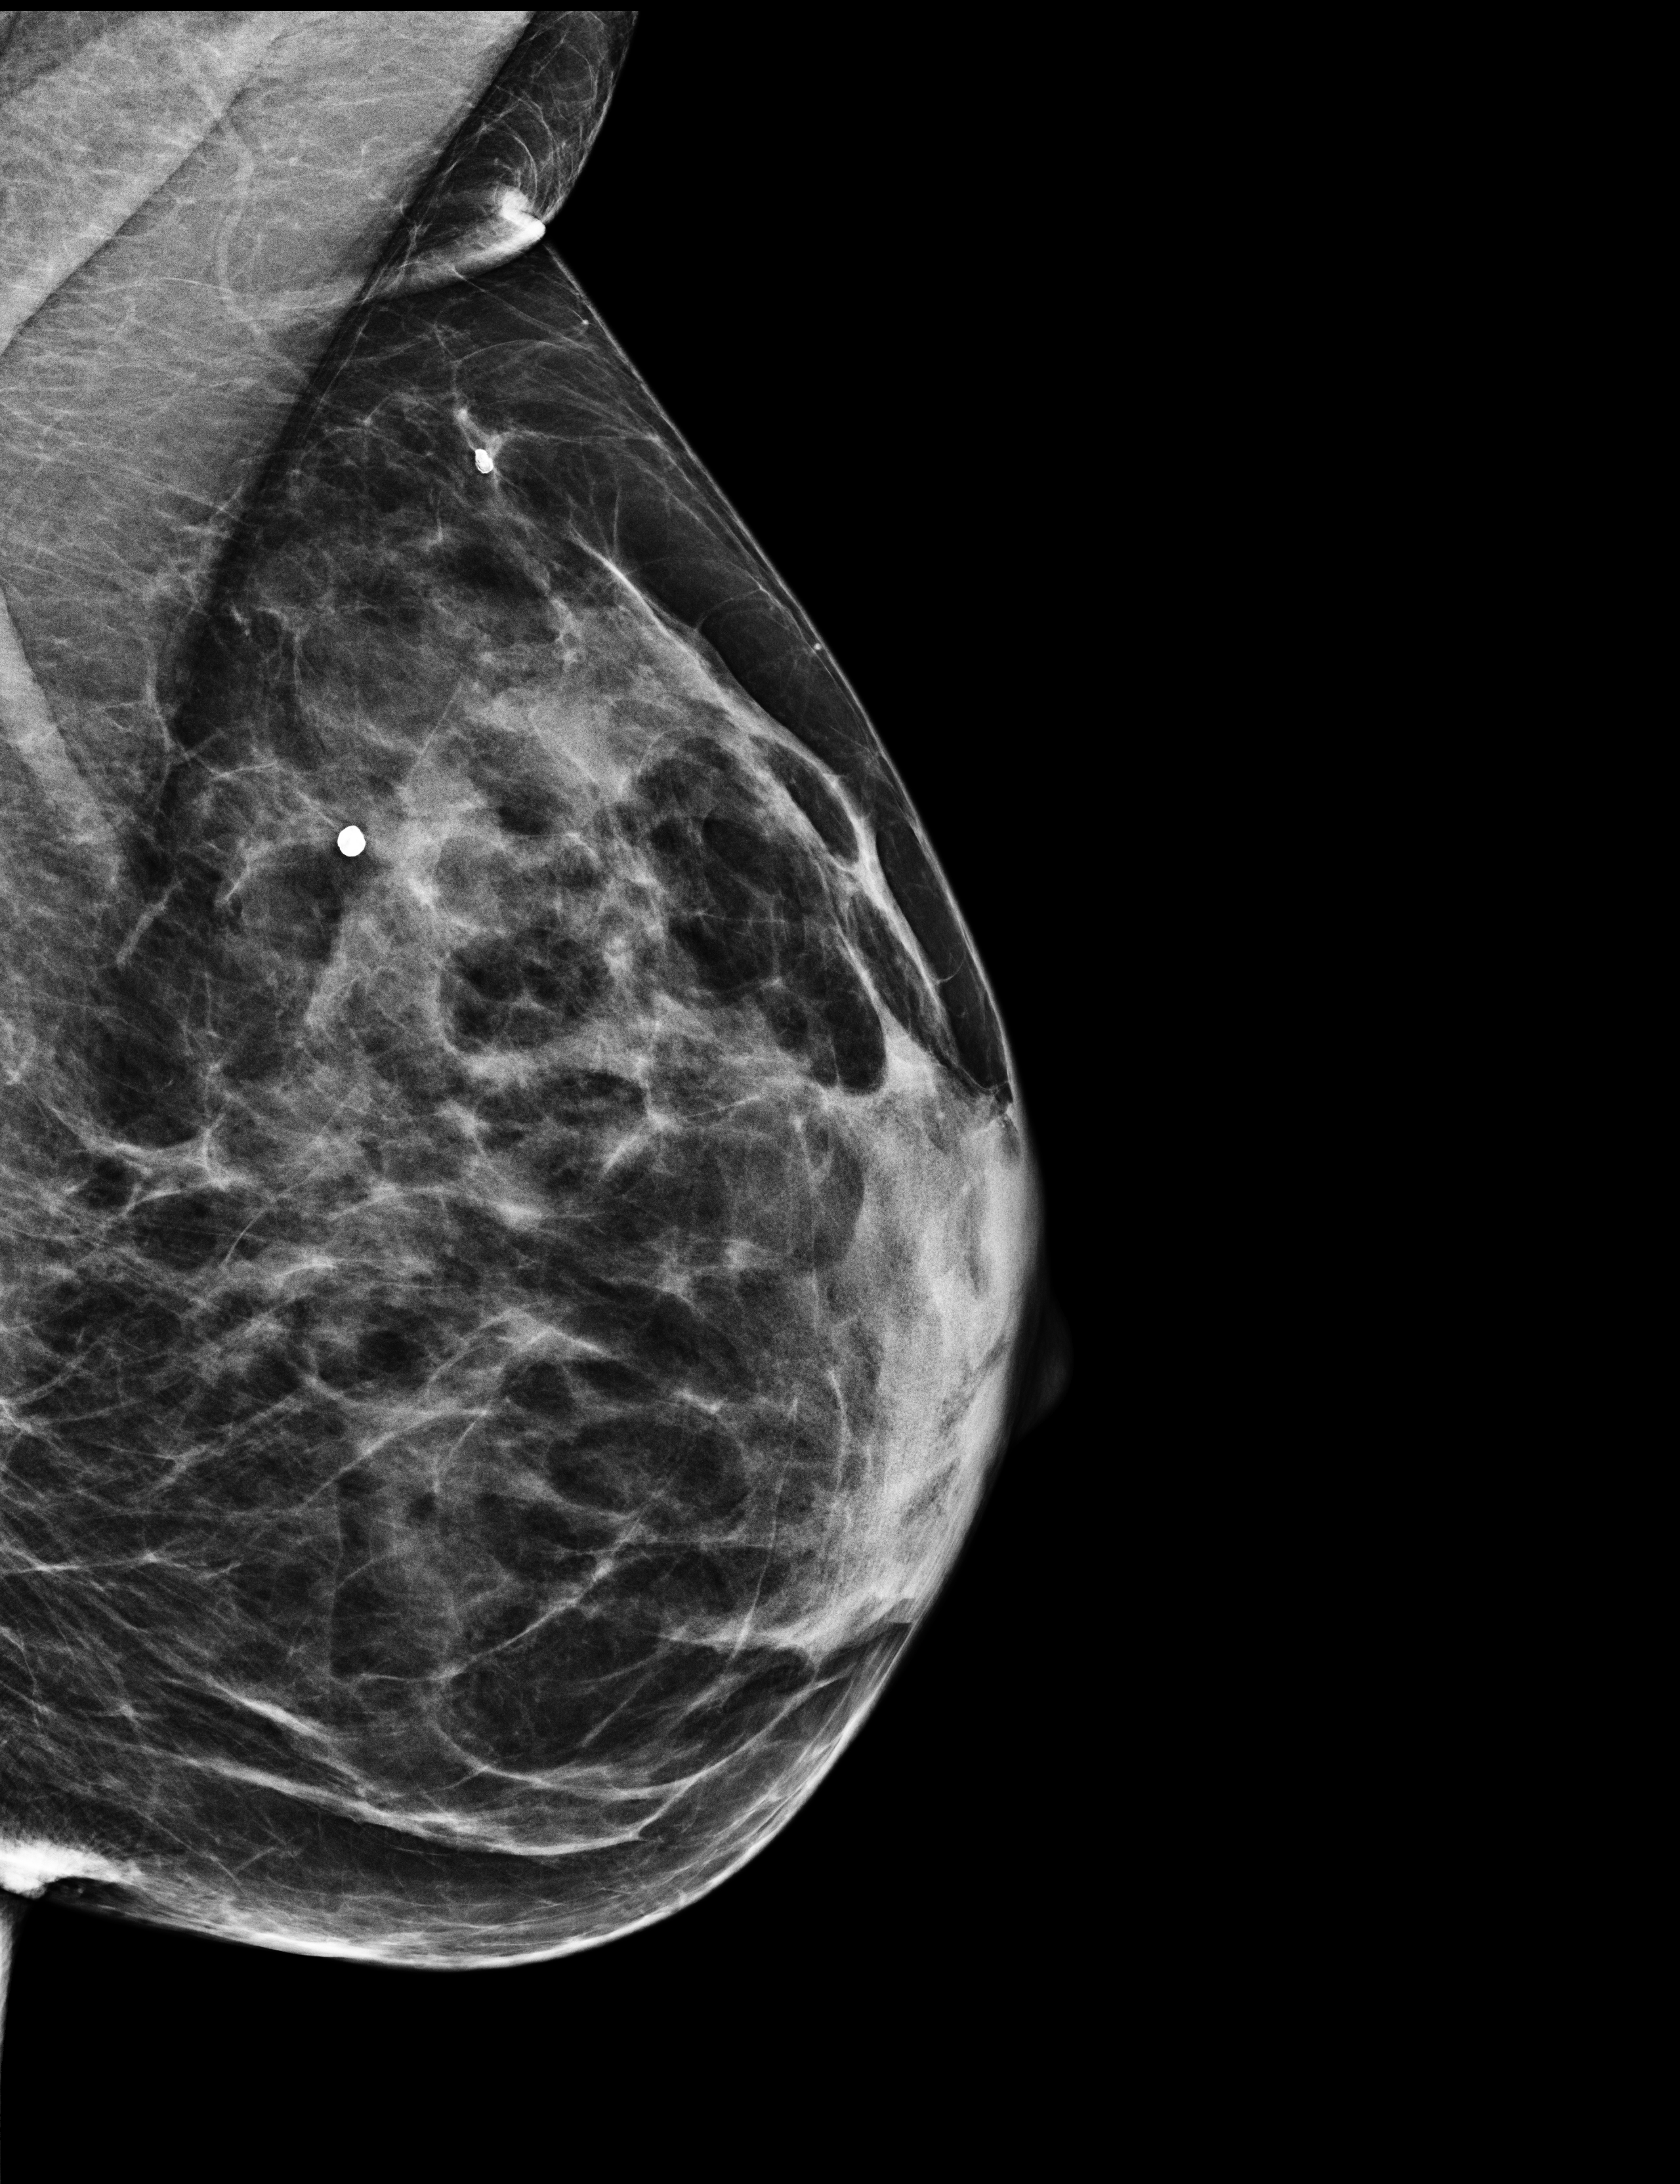
Screening examination; compressed breast thickness 45 mm. Patient: female, 55 years.
Image type: full-field digital mammogram. Breast: left. Projection: MLO view.